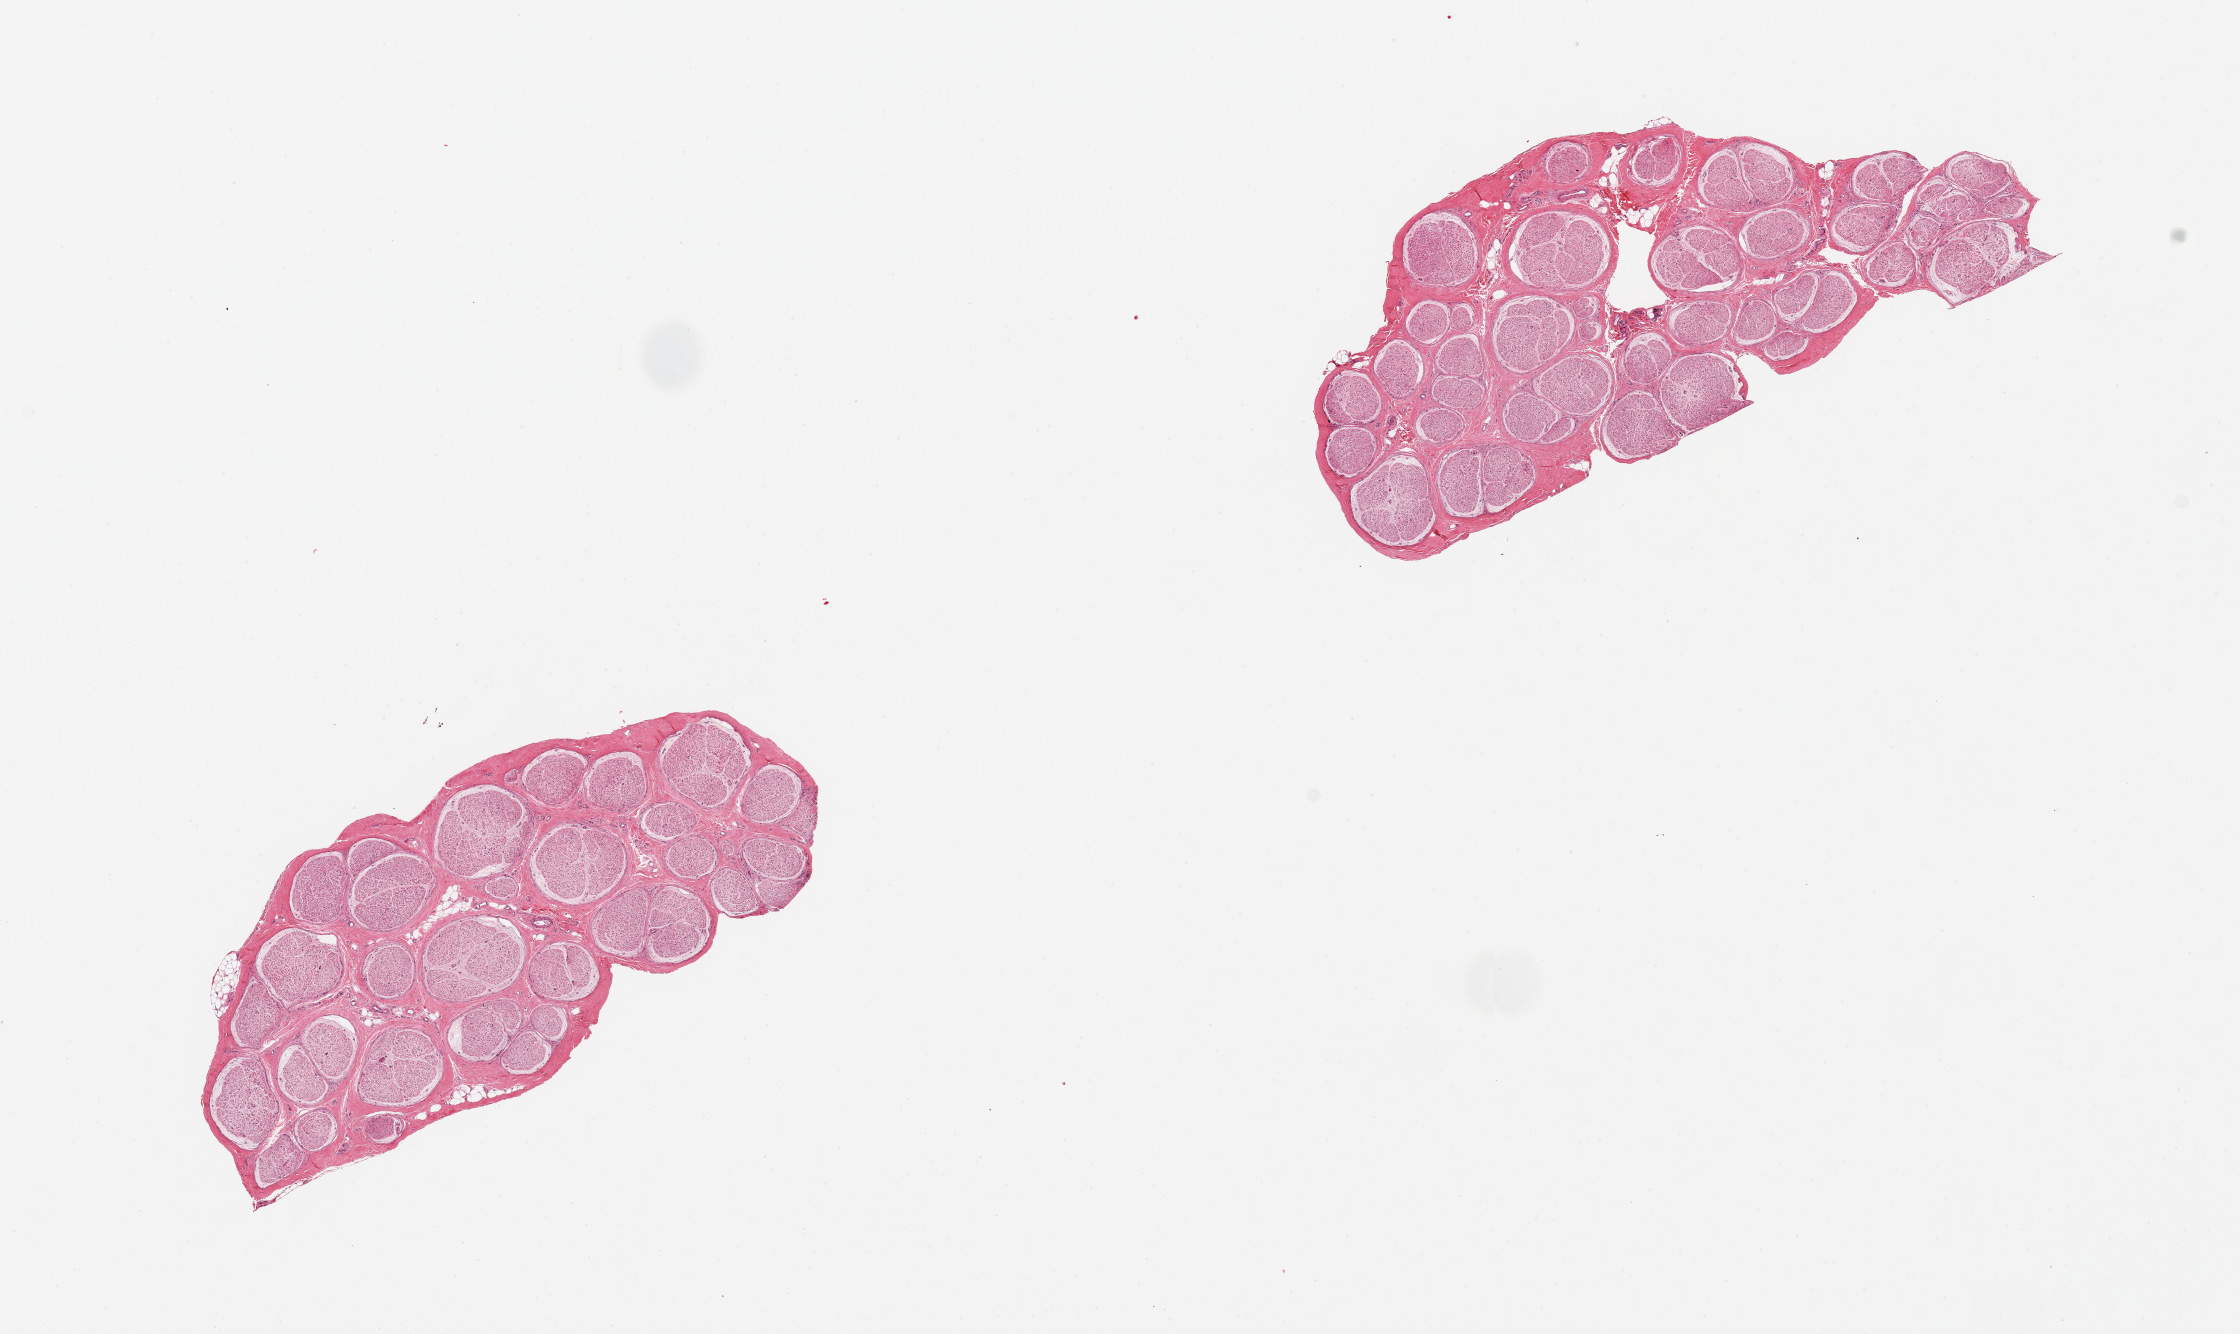
Haematoxylin and eosin whole-slide image, brightfield, shown as a low-resolution overview of the whole scanned area (about 17.7 x 10.6 mm, from a 20x scan); PAXgene-fixed paraffin-embedded (PFPE) section; target tissue: tibial nerve; tissue donor sample. Donor: male.
Reviewer comment on this tissue sample: 2 pieces; well trimmed.